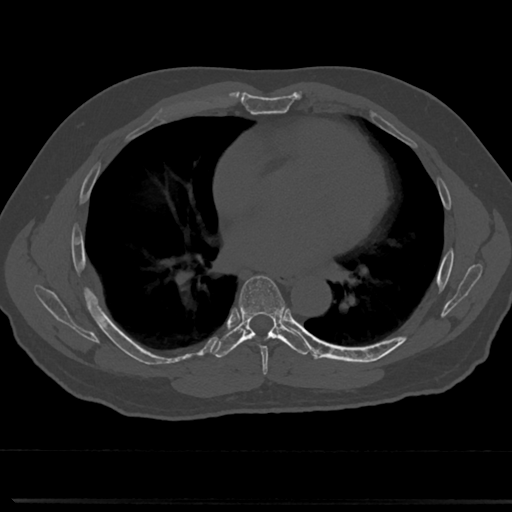
CT including the spine, one axial slice. Position 419 of 817 along the scan axis. Reconstruction kernel Br40s/3. 120 kVp. Bone window (W 1800 / L 400 HU). 0.5 mm slice thickness. 512 × 512 image matrix, field of view 355 × 355 mm. Patient: male, 61 years. From the clinical record (not read from this slice): primary cancer: prostate.
Structures marked on this image (semi-automatic segmentation, software-assisted and operator-edited):
- T6 vertebra: bounding box <241,281,286,361> (left, top, right, bottom; pixels)
- T7 vertebra: <239,275,286,335>